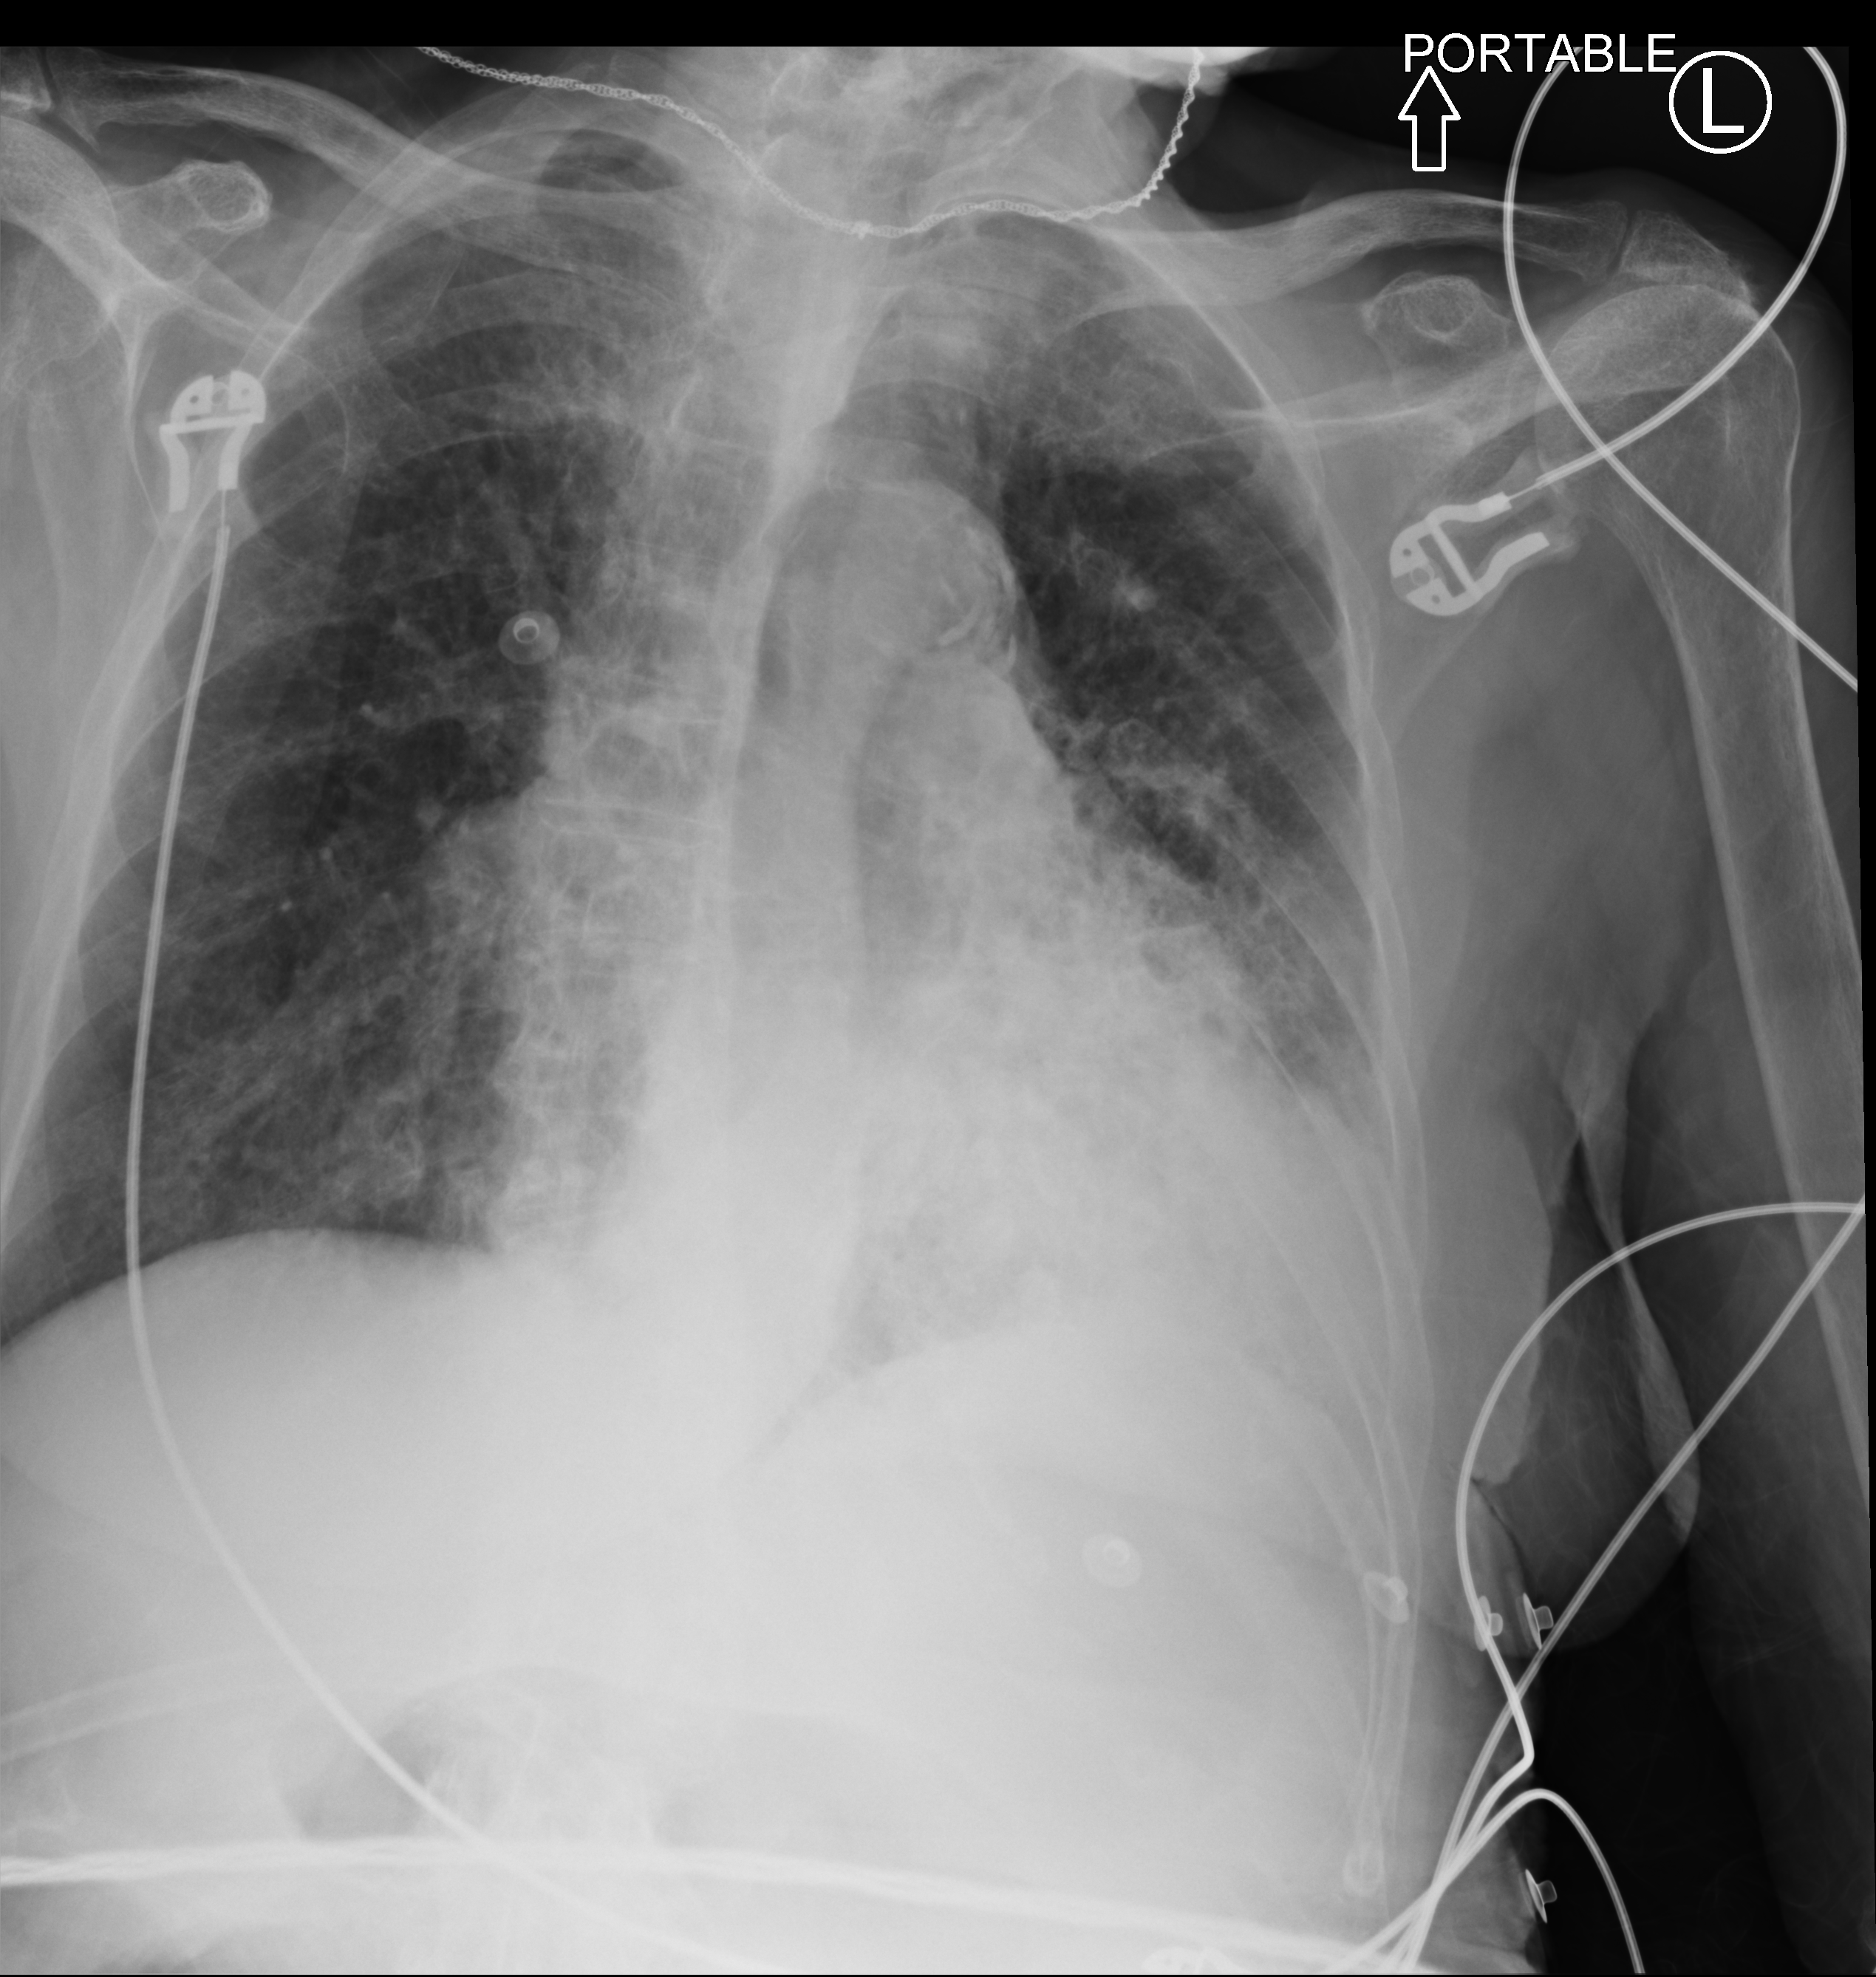
Chest X-ray (portable); anteroposterior (AP) projection. Female patient hospitalised with COVID-19, age 75–90 years.
Admission-level facts for this patient (not findings on this image; timing relative to this image not recorded): hypertension (admission record): yes; smoking status (admission record): former; admitted to intensive care during this hospital stay: yes.